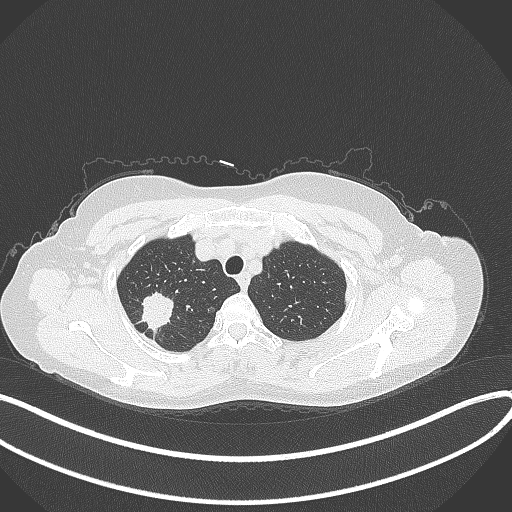
Chest CT, one axial slice. Position 308 of 337 along the scan axis. Reconstruction kernel B70f. 120 kVp. Lung window (W 1500 / L -600 HU). 1 mm slice thickness. 512 × 512 image matrix, field of view 400 × 400 mm. Female patient, age 50 years. From the clinical record (not read from this slice): clinical TNM (as recorded): T1c N0 M0; histopathological grade: G2-3.
Structures marked on this image (bounding box drawn by a radiologist):
- lung tumour (recorded histology: adenocarcinoma): bounding box [x1, y1, x2, y2] px = [136, 287, 177, 334]